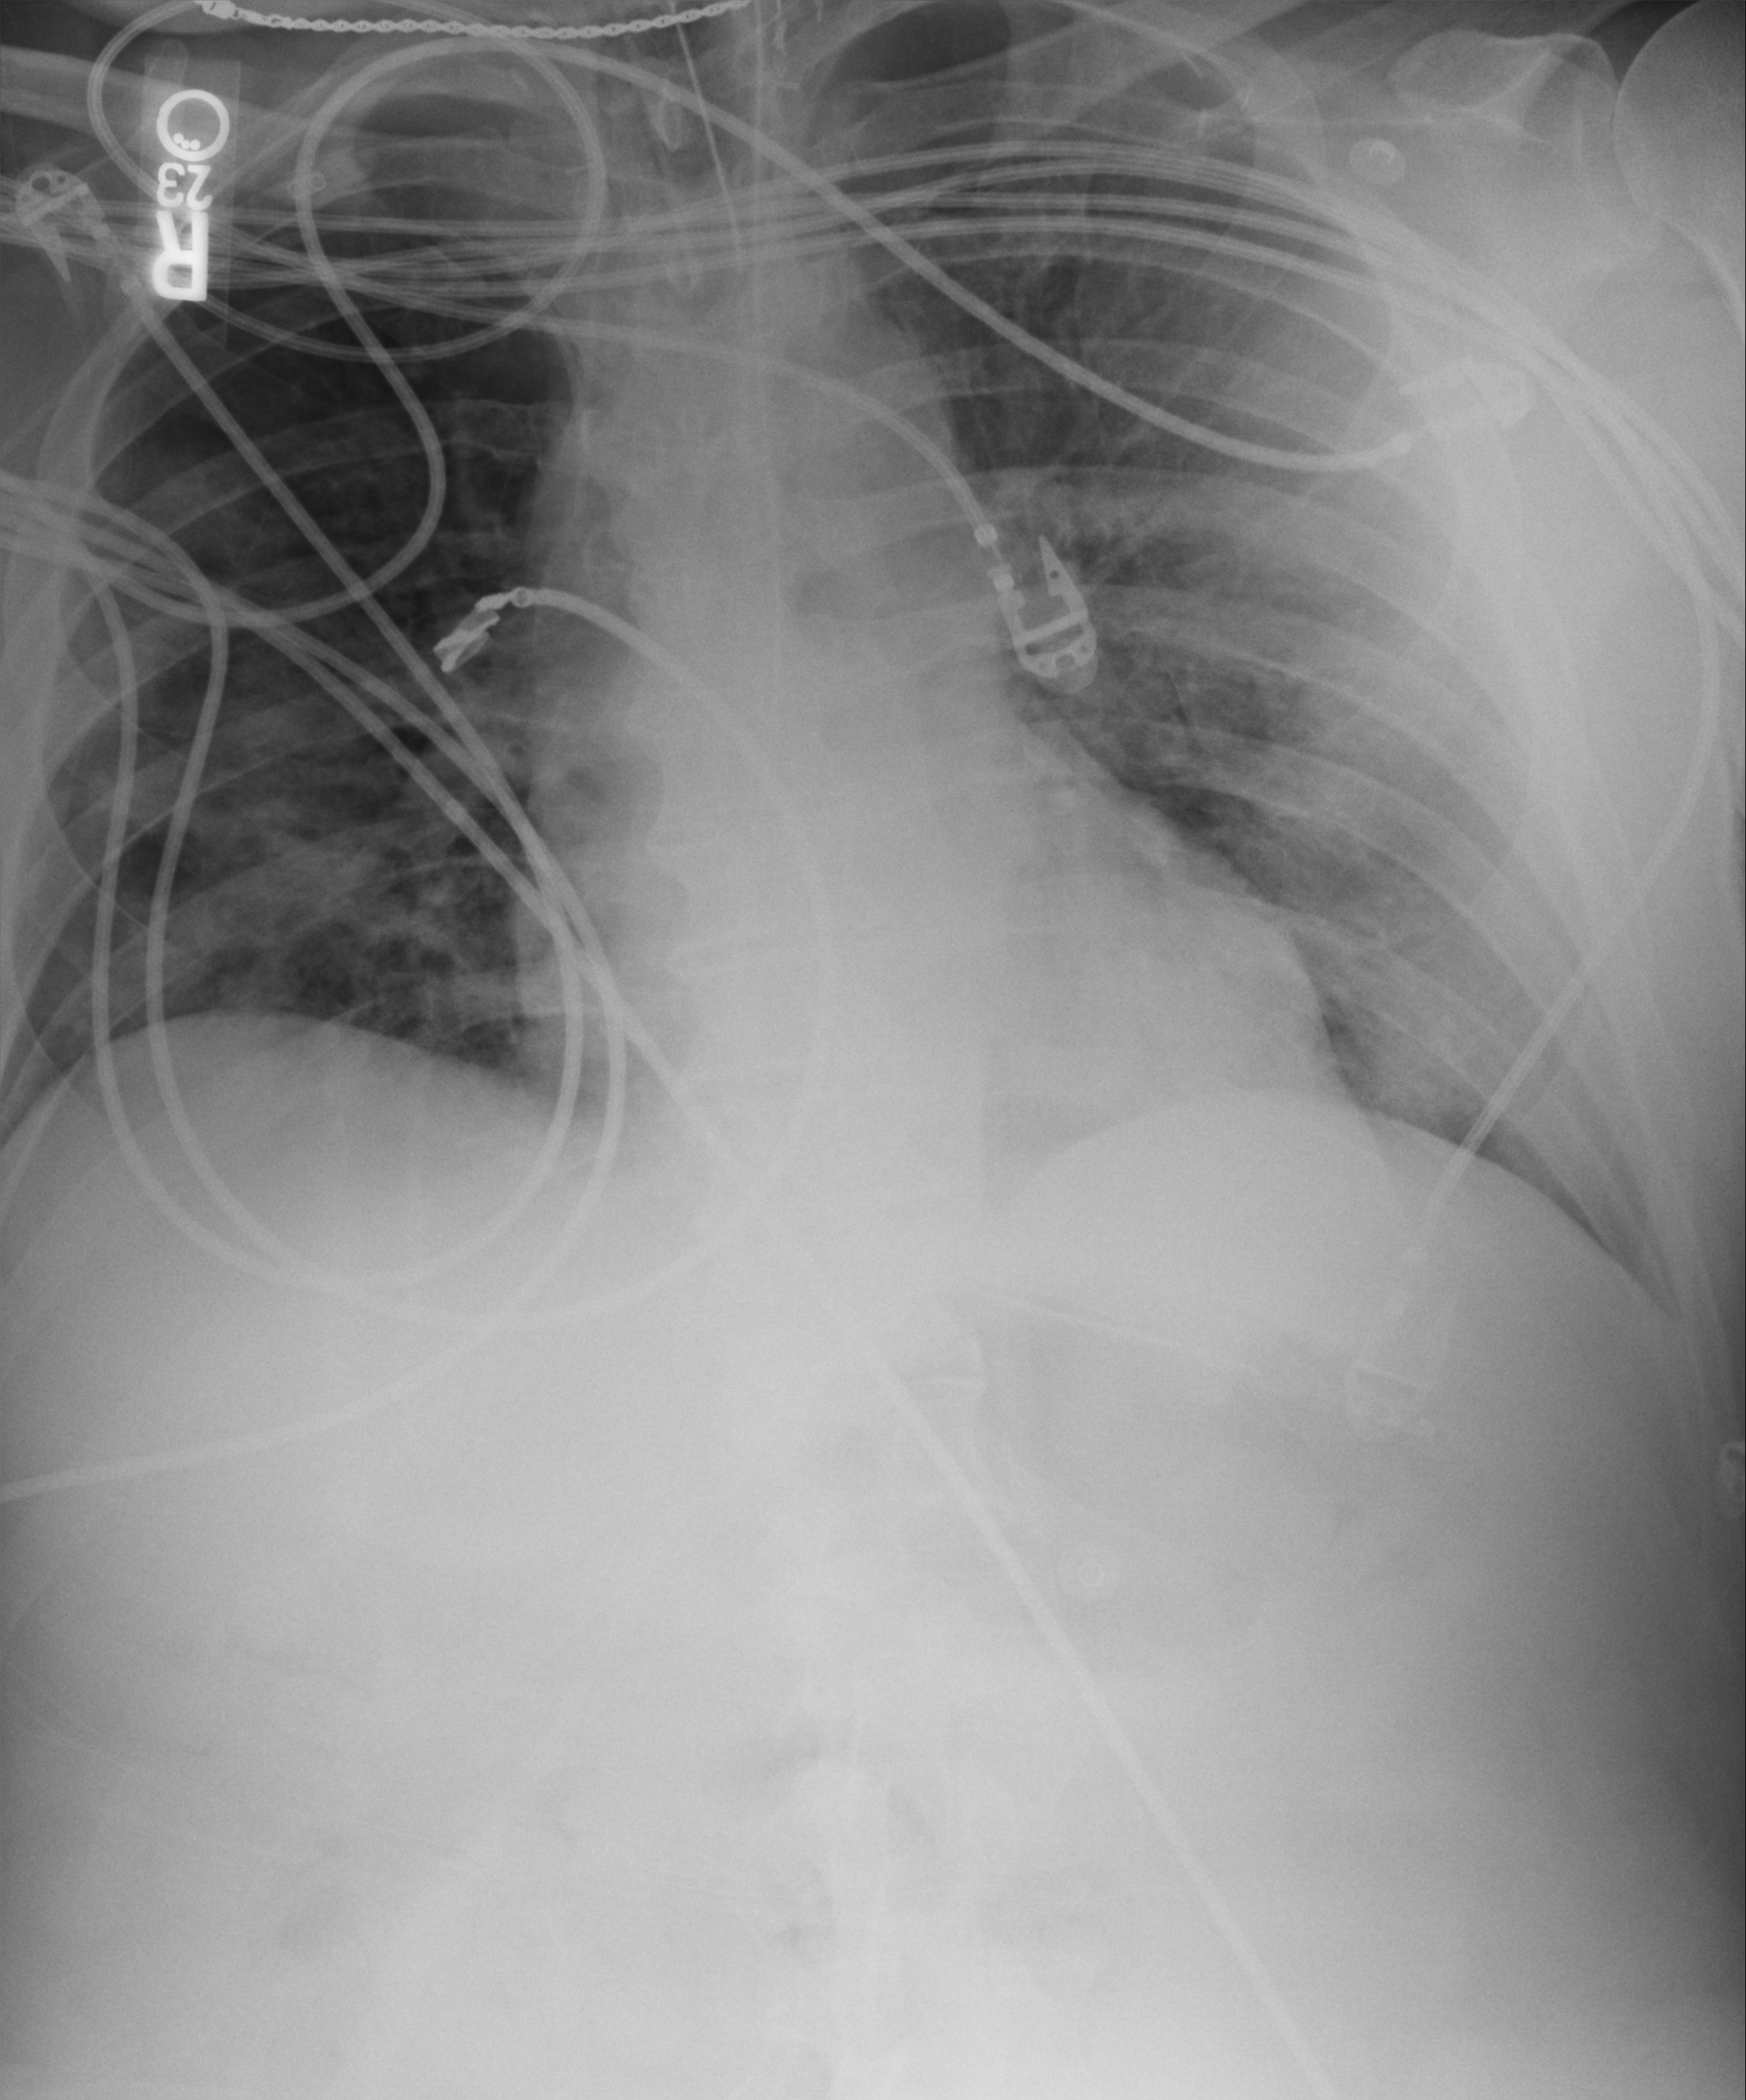
Bedside chest radiograph (computed radiography); anteroposterior (AP) projection. Adult patient hospitalised with COVID-19, age 18–59 years.
From the hospital-stay record, not from the radiograph (when in the stay this image was taken is not recorded):
- length of hospital stay: 19 days
- mechanically ventilated during this hospital stay: yes
- admitted to intensive care during this hospital stay: yes